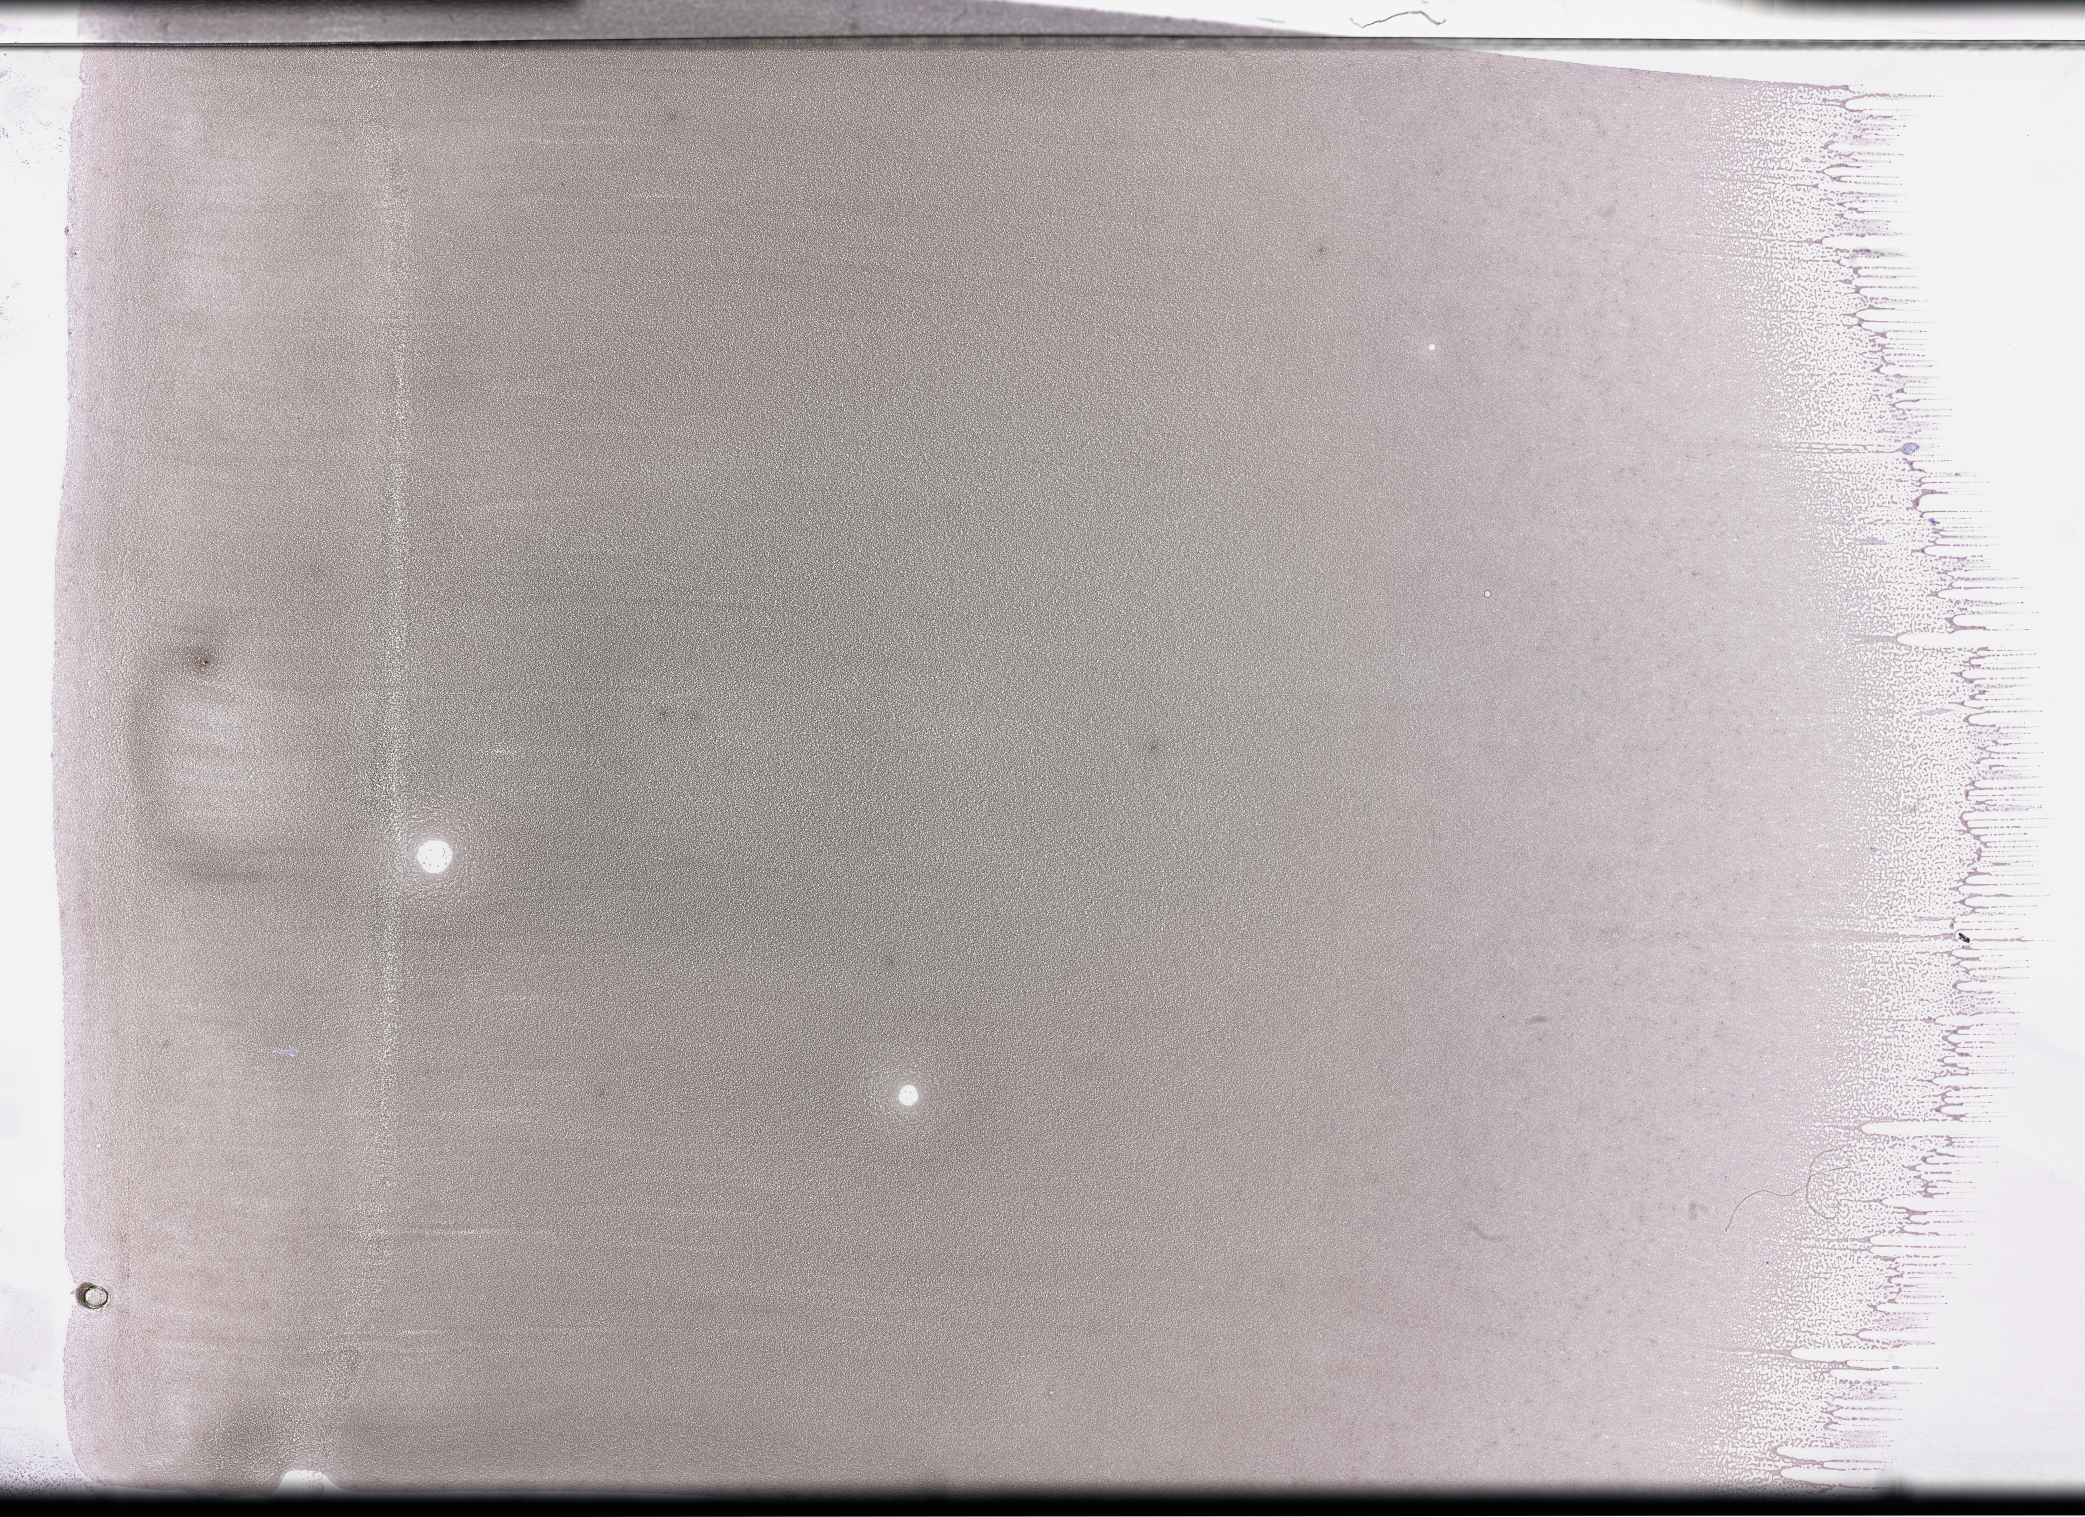
Whole-slide image of a whole blood smear, Wright–Giemsa stain — whole scanned area (about 33.7 x 24.5 mm) shown as a low-resolution overview. EDTA-anticoagulated smear. Specimen time point: collected on treatment. Female patient.
From a patient with: Plasma Cell Myeloma.